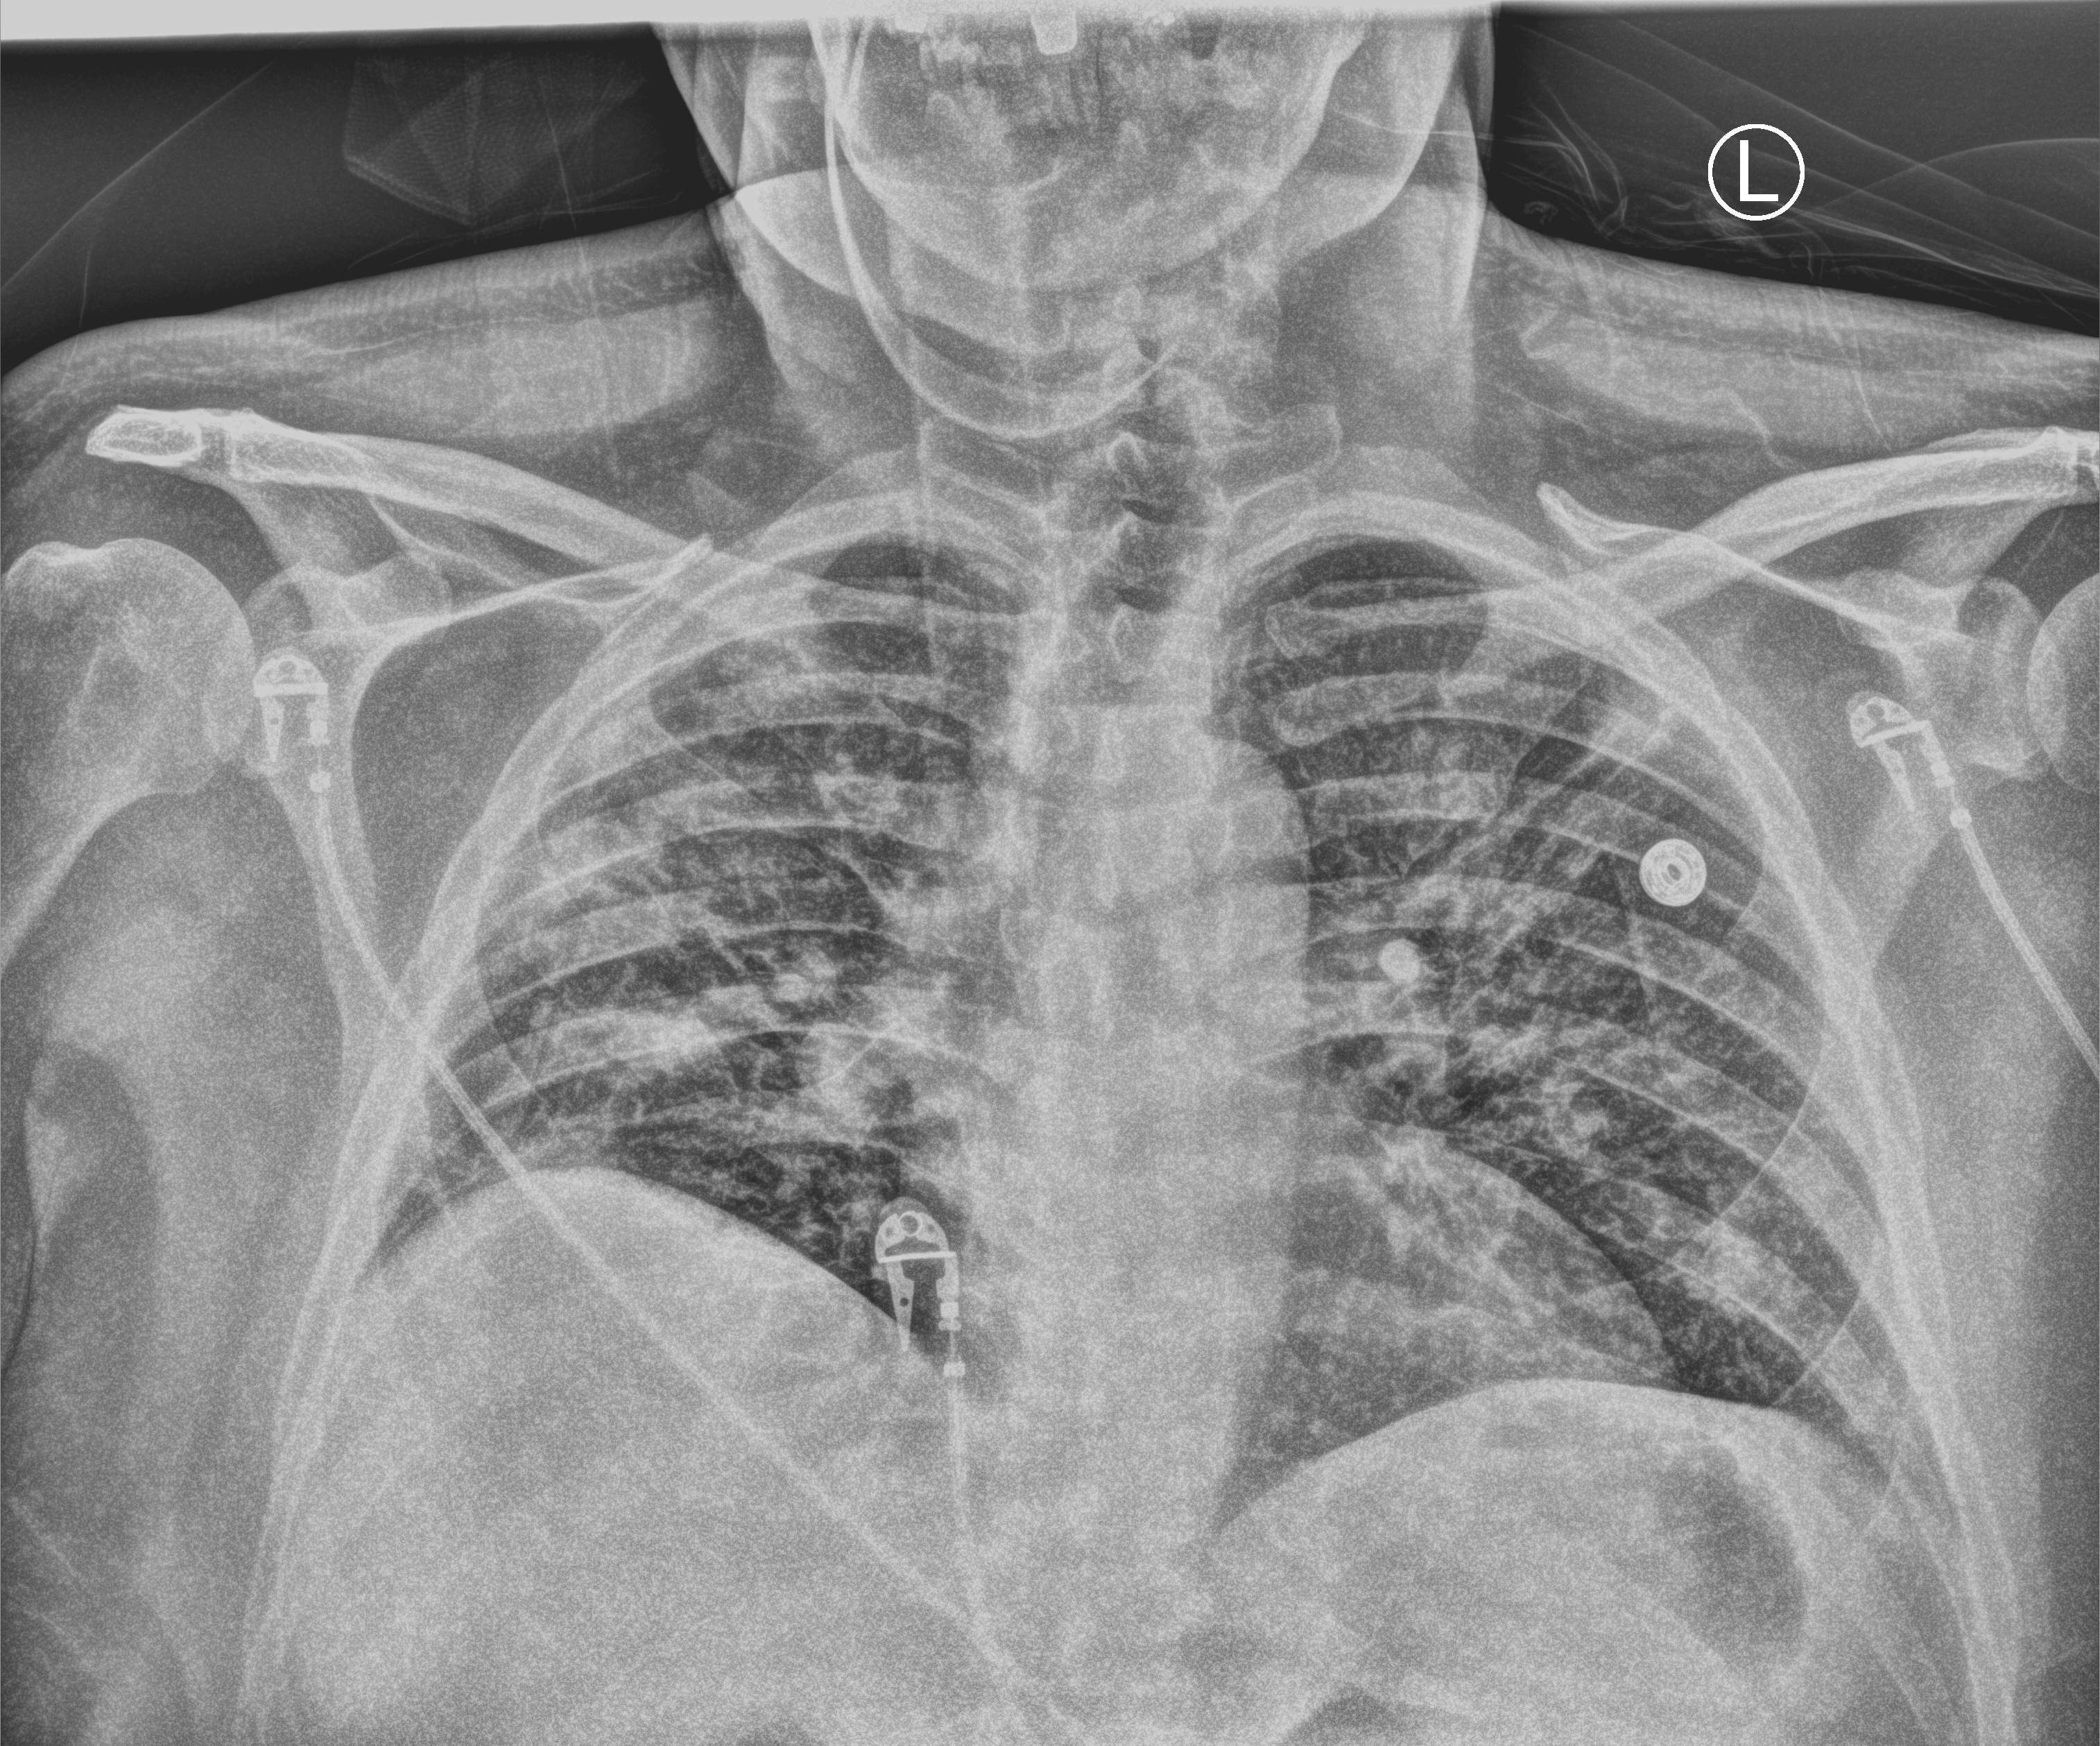
Bedside chest radiograph (computed radiography), anteroposterior (AP) projection. Male patient hospitalised with COVID-19, age 18–59 years.
Admission-level facts for this patient (not findings on this image; timing relative to this image not recorded):
- chronic kidney disease (admission record): no
- admitted to intensive care during this hospital stay: yes
- mechanically ventilated during this hospital stay: yes